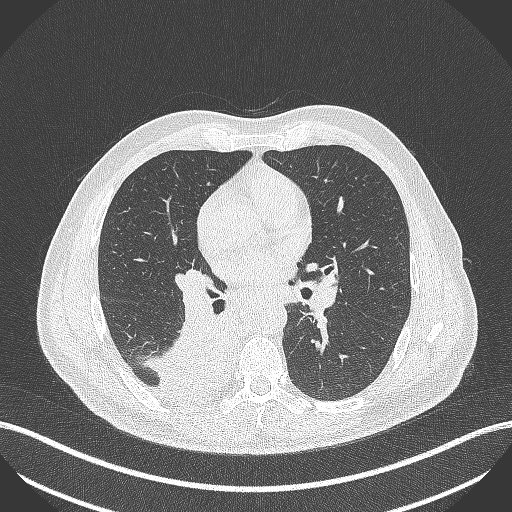
Chest CT, one axial slice. Slice 252 of 451 in the series (ordered by position). Reconstruction kernel B70f. Lung window (W 1500 / L -600 HU). 512 × 512 image matrix, field of view 400 × 400 mm. Patient: male, 61 years. Case-level facts recorded for this patient, not image findings: clinical TNM (as recorded): T1 N0 M0.
Annotated regions visible in this slice (bounding box drawn by a radiologist):
- lung tumour (recorded histology: small cell carcinoma): bounding box [x1, y1, x2, y2] px = [153, 309, 235, 407]